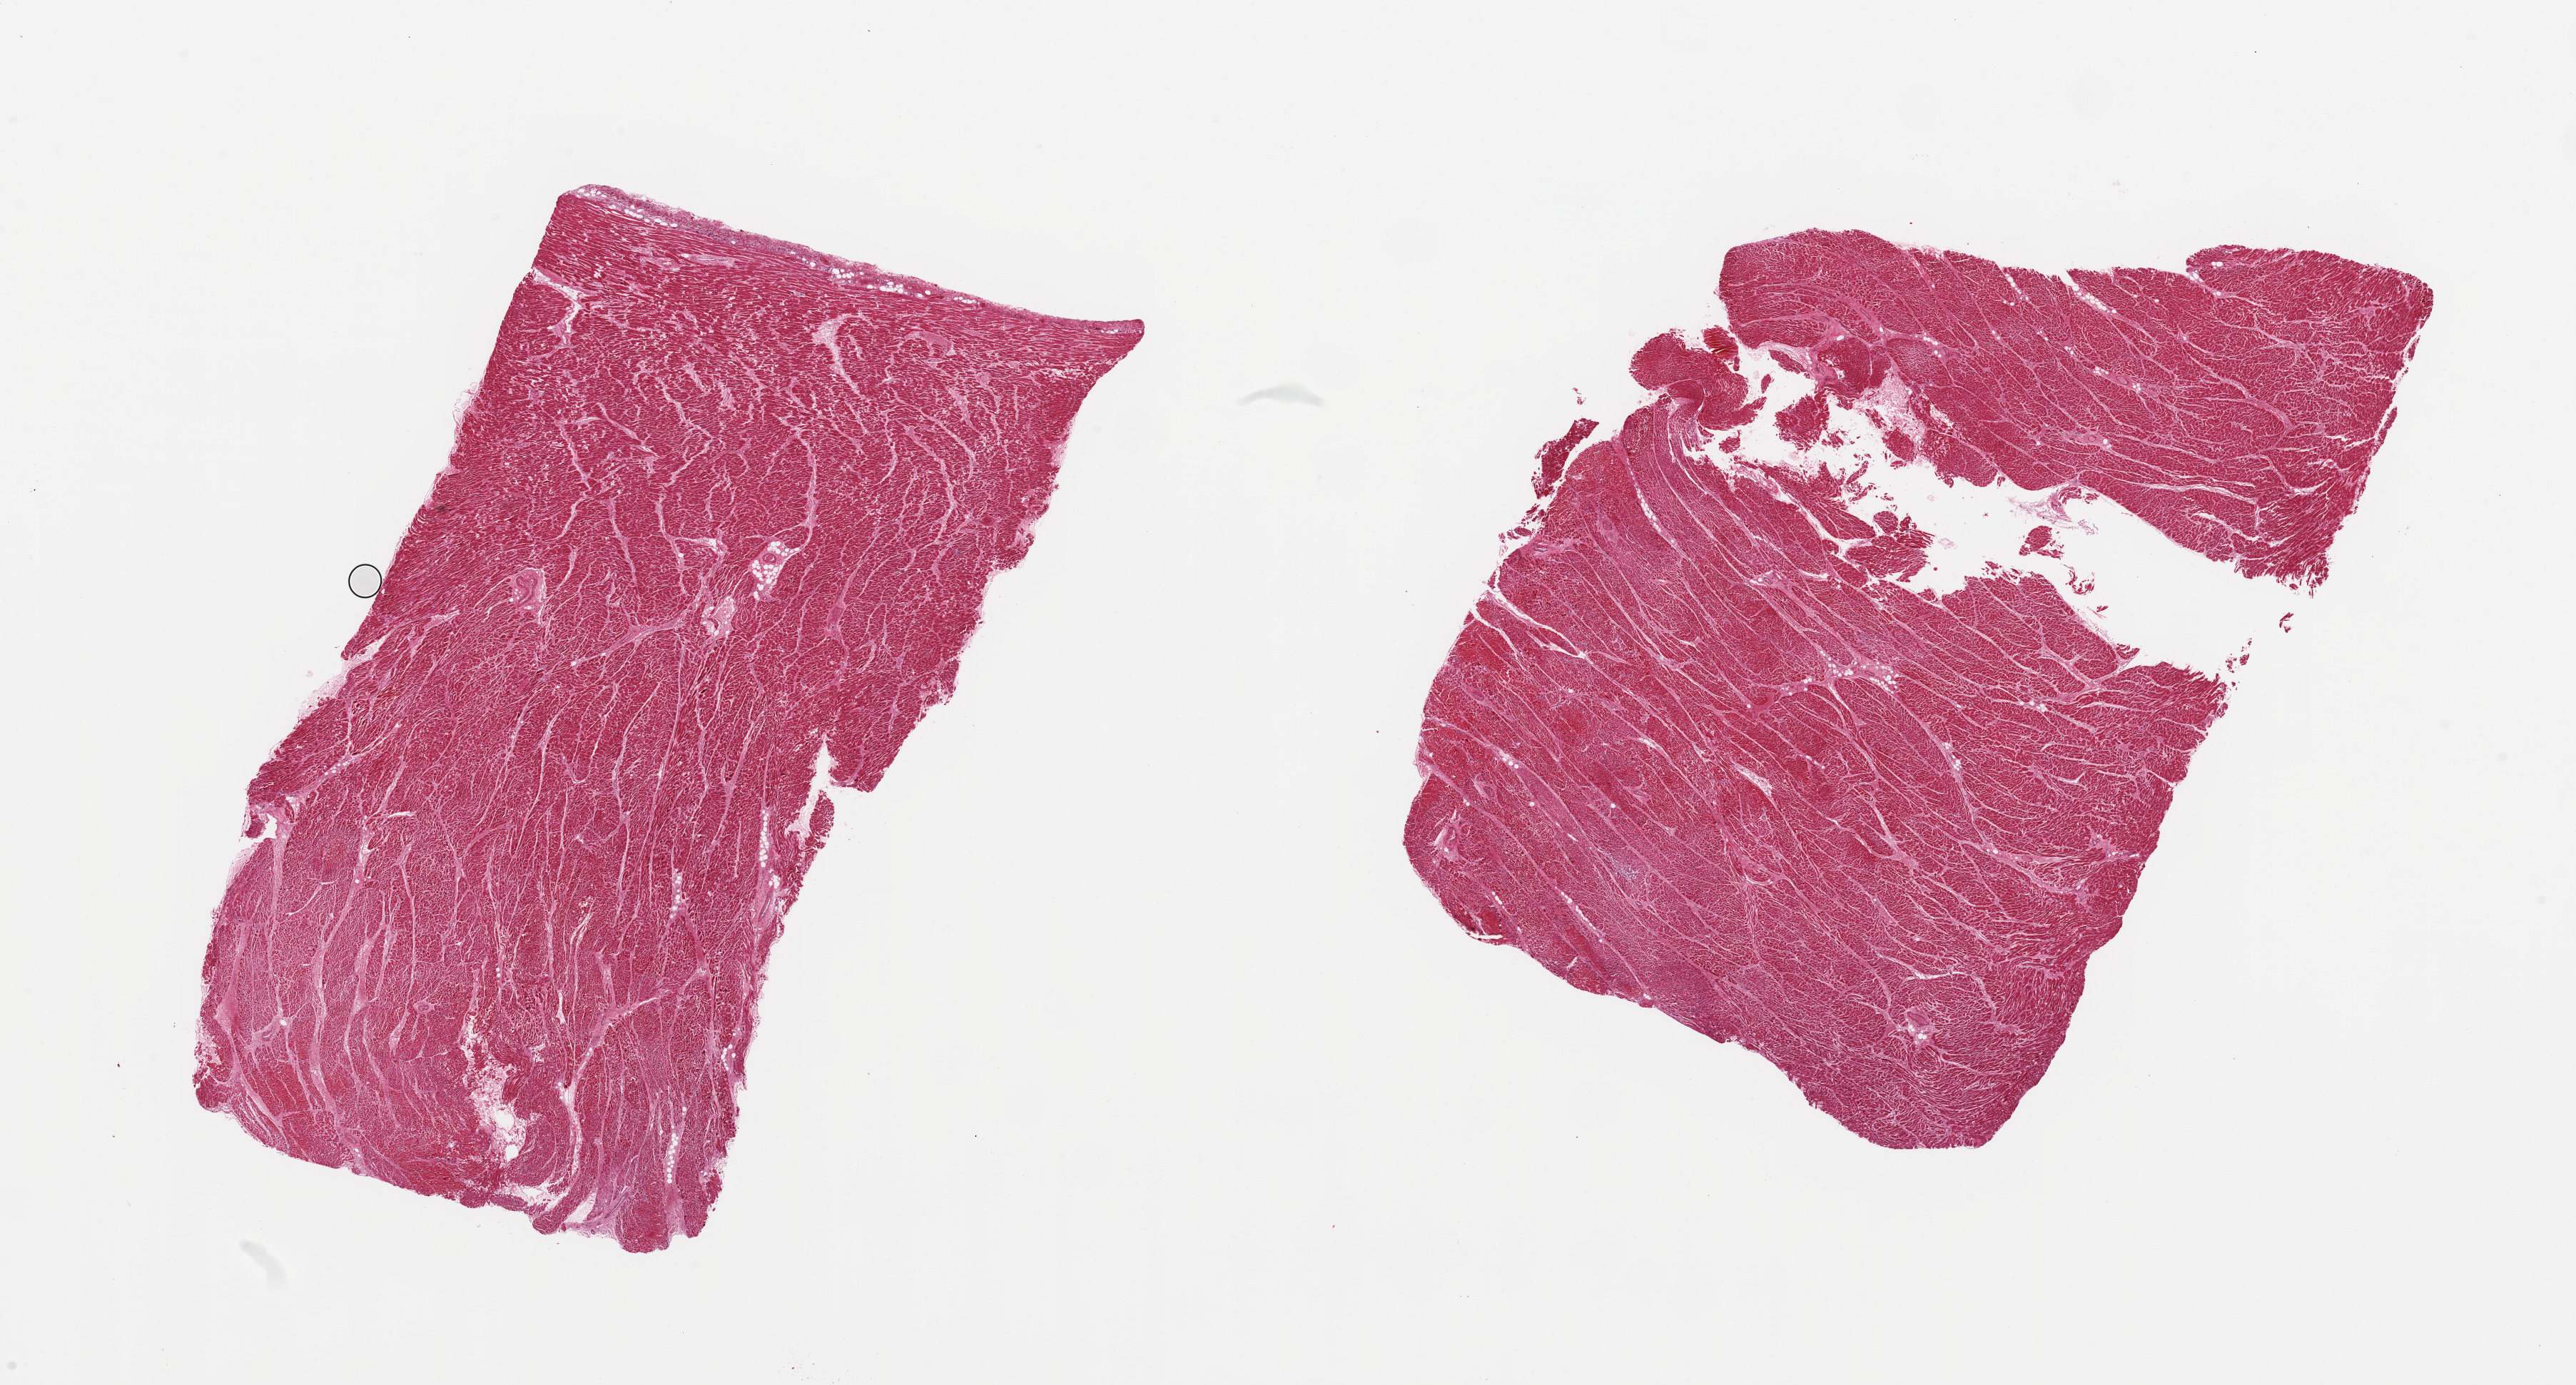
Hematoxylin and eosin (H&E) whole-slide image, a low-resolution overview of the entire scanned area, about 28.5 x 15.3 mm, PAXgene-fixed paraffin-embedded (PFPE) section, section of heart (target tissue), tissue donor sample. Donor: male.
Pathologist's review note for this sample: 2 pieces, moderate interstitial fibrosis/ chronic ischemic changes.